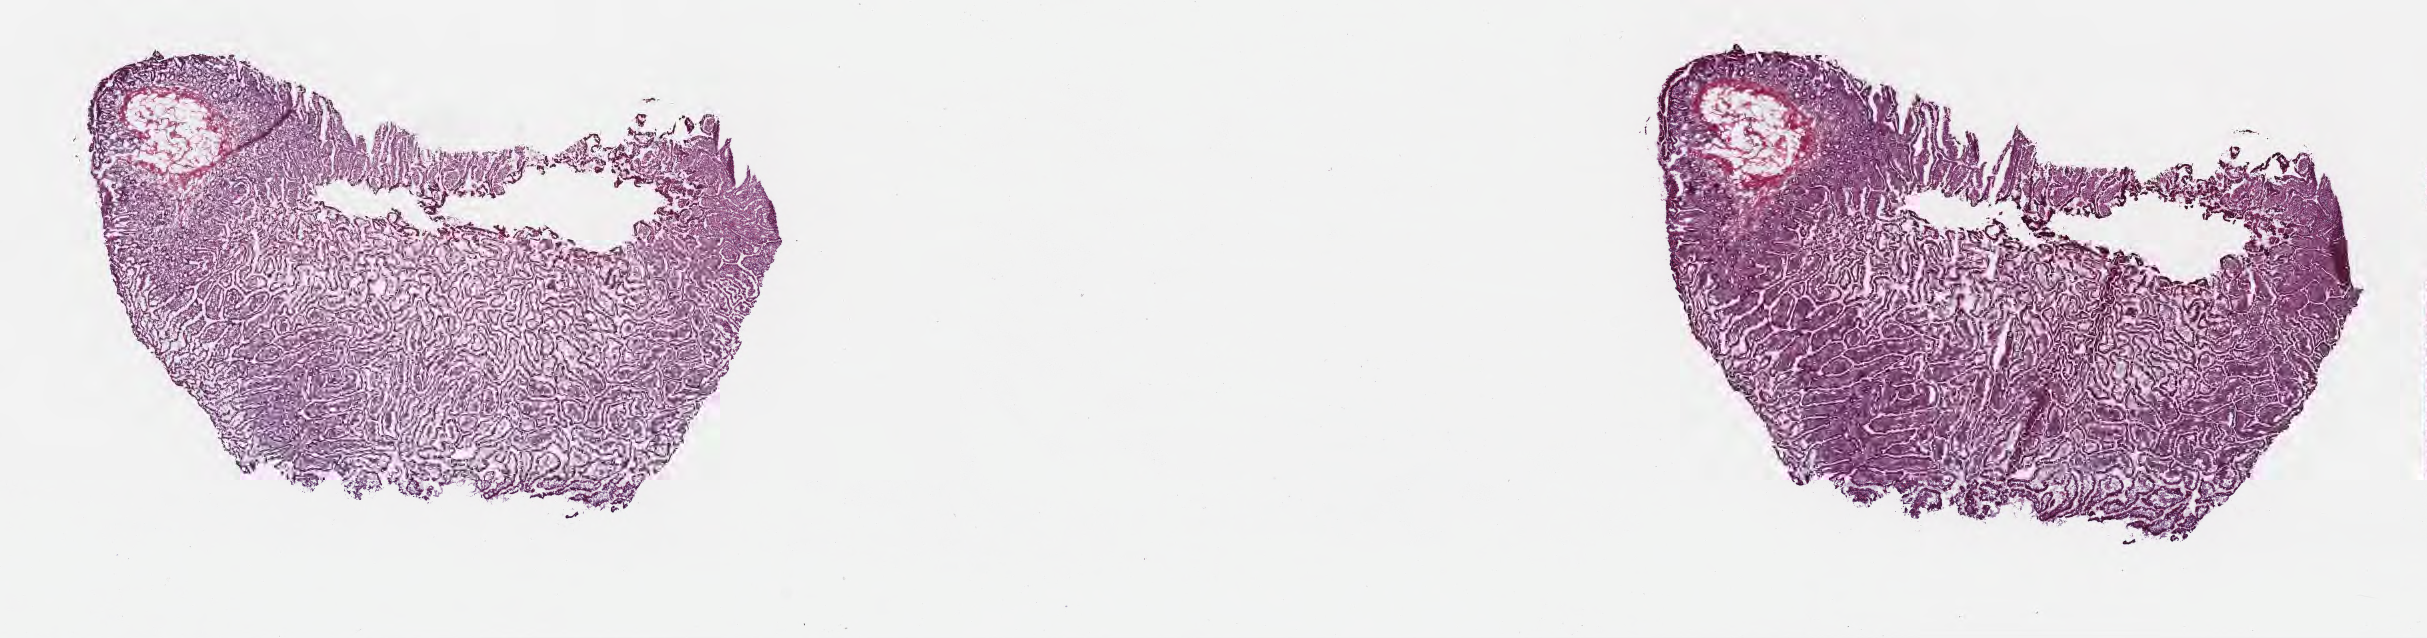
Whole-slide image, hematoxylin and eosin (H&E) stain, shown as a low-resolution overview of the whole scanned area (about 19.6 x 5.2 mm). Cryosection. Non-tumor (normal tissue) sample from a patient with infiltrating duct carcinoma, NOS. Anatomic site: head of pancreas. Female, age 73 years at initial diagnosis. Composition of this section per pathologist review: tumor cells 0%, tumor nuclei 0%, stromal cells 0%, necrosis 0%, normal cells 100%. Inflammatory infiltration, as recorded: lymphocyte infiltration 0%, monocyte infiltration 0%, neutrophil infiltration 0%.
This section: non-tumor tissue sample; the patient's diagnosis is given above.